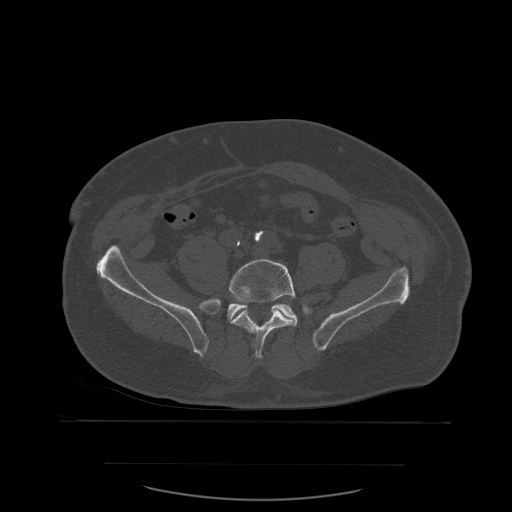
CT including the spine, one axial slice. Slice 133 of 590 in the series (ordered by position). Bone window (W 1800 / L 400 HU). 512 × 512 image matrix, field of view 479 × 479 mm. Patient age 71 years. Case-level facts recorded for this patient, not image findings: primary cancer: lung; vertebrae with lytic lesions (as recorded): T1, T2, L5, S1.
Outlined on this slice (semi-automatic segmentation, software-assisted and operator-edited):
- L5 vertebra: bounding box [x1, y1, x2, y2] px = [229, 259, 298, 359]